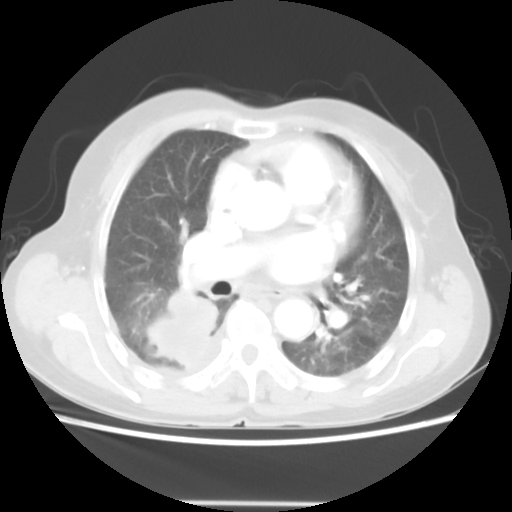
Chest CT, one axial slice. Slice 28 of 52 in the series (ordered by position). Lung window (W 1500 / L -600 HU). 5 mm slice thickness. 512 × 512 image matrix, field of view 337 × 337 mm. Patient: female, 67 years. From the clinical record (not read from this slice): clinical TNM (as recorded): T3 N1 M1.
Structures marked on this image (bounding box drawn by a radiologist):
- lung tumour (recorded histology: adenocarcinoma): box from (x=148, y=288) to (x=224, y=375) px